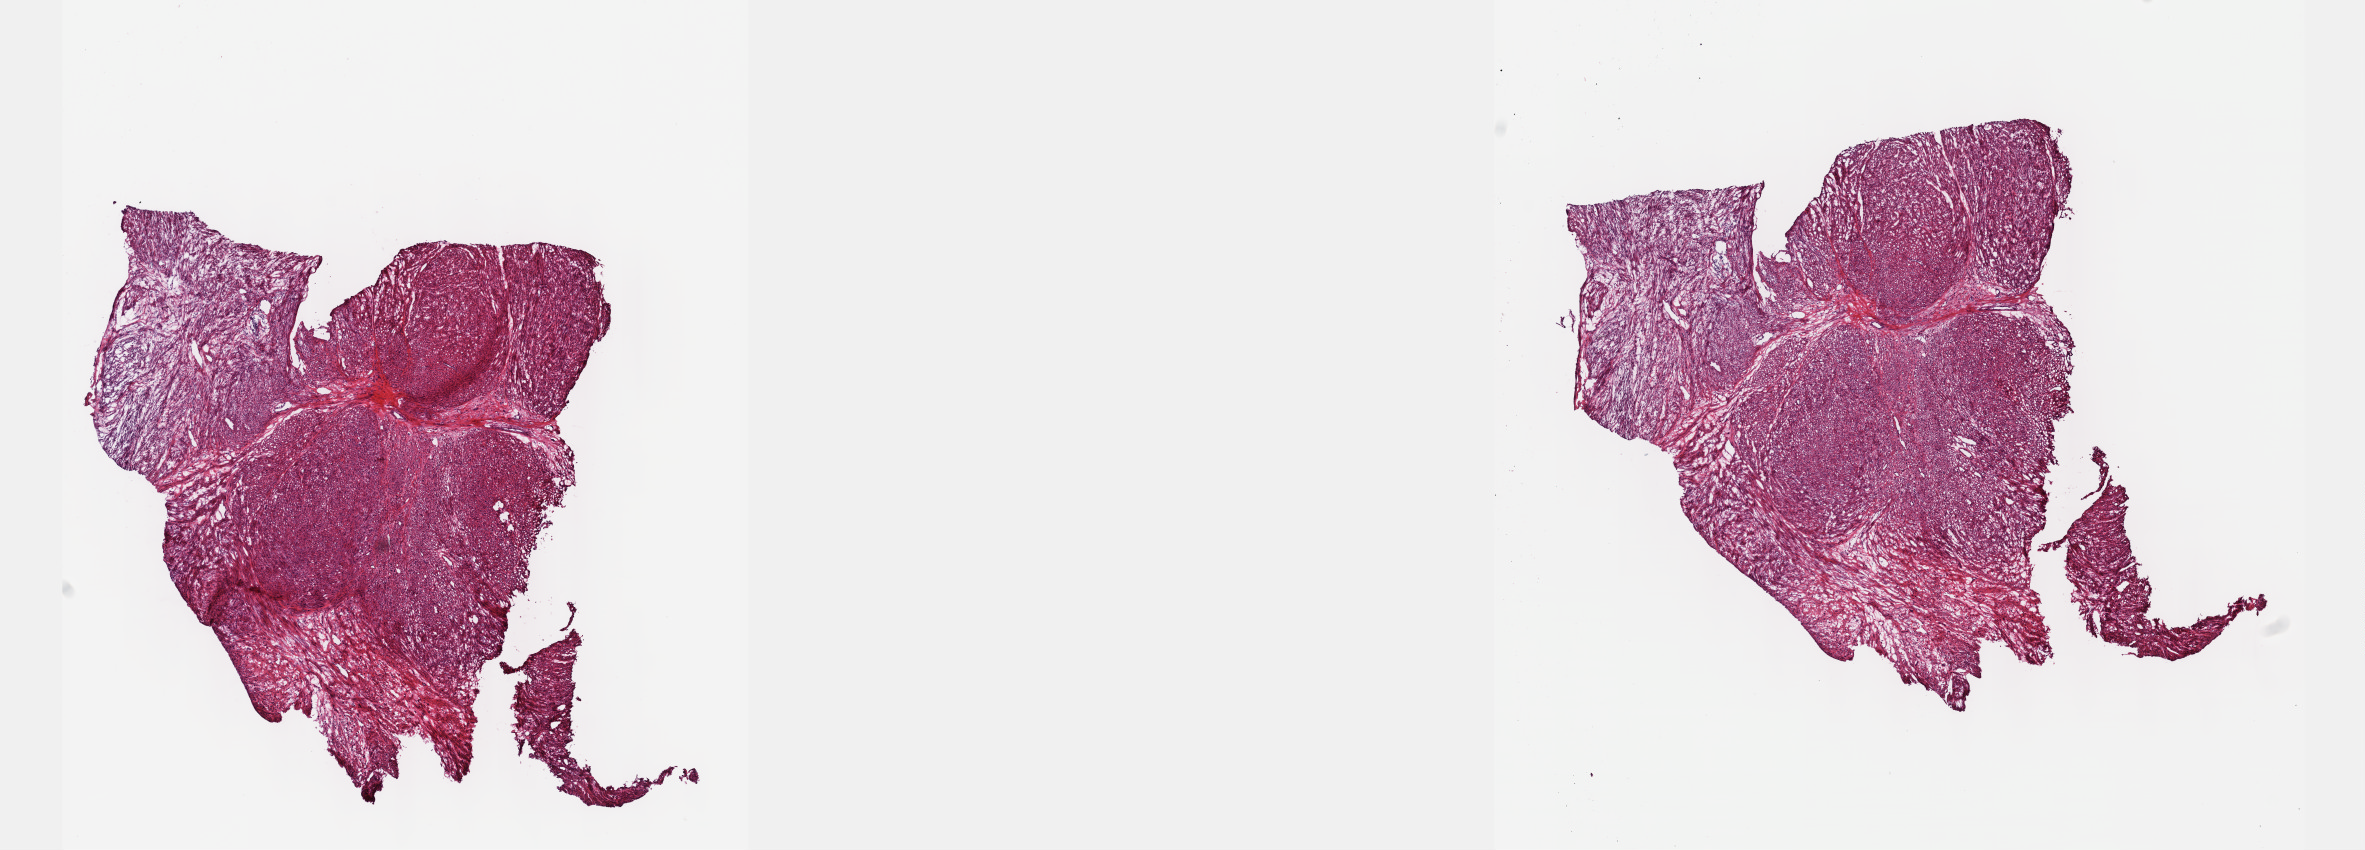
H&E whole-slide image, shown as a low-resolution overview of the whole scanned area (about 19.1 x 6.9 mm). Frozen section. Sample: primary tumour, connective, subcutaneous and other soft tissues. Female patient. Slide review estimates, as recorded: tumour cells 100%, tumour nuclei 80%, normal cells 0%, stromal cells 0%, necrosis 0%. Infiltration values recorded for this section: lymphocyte infiltration 1%, monocyte infiltration 0%, neutrophil infiltration 0%.
- diagnosis: Leiomyosarcoma, NOS (connective, subcutaneous and other soft tissues of thorax)